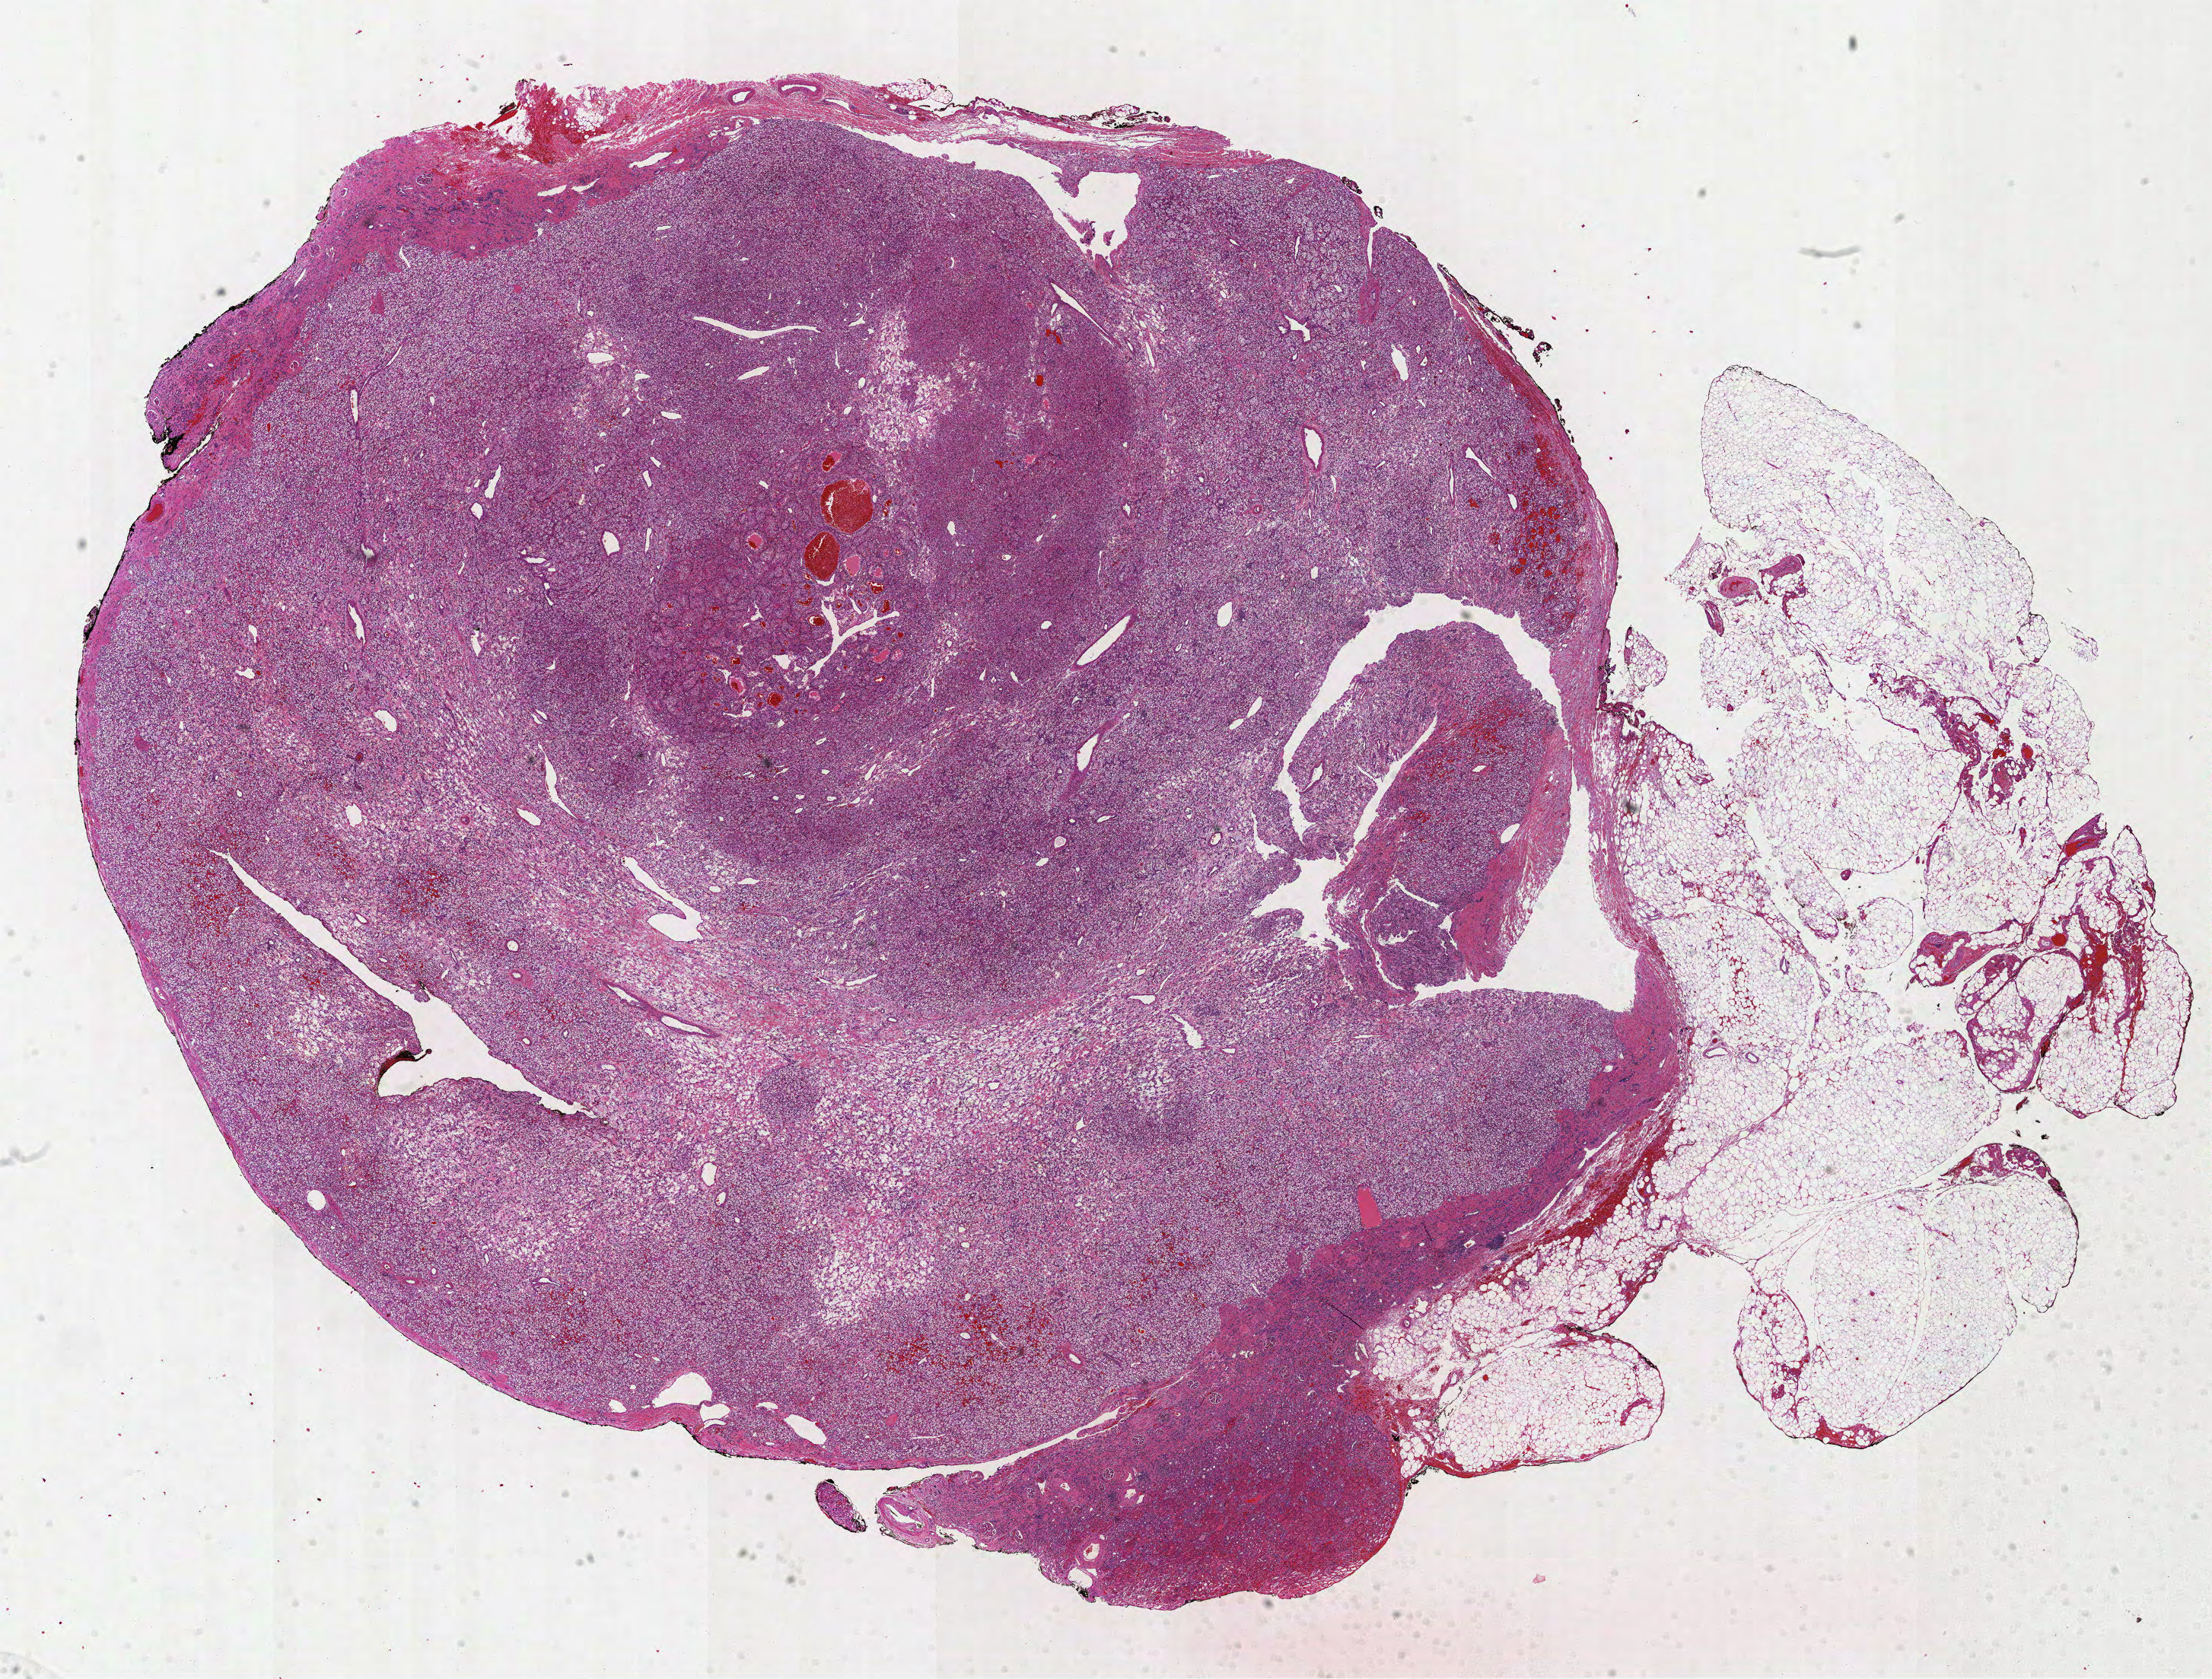
Digitized Hematoxylin and eosin (H&E) stained tissue section (whole slide) — low-resolution overview of the scanned area, about 23.4 x 17.8 mm (from a 40x scan), formalin-fixed paraffin-embedded (FFPE) diagnostic section, primary tumour sample from the kidney. Patient: female, age at initial diagnosis 67 years. Histologic grade: G2 (moderately differentiated).
- AJCC pathologic stage: I
- laterality: right
- histologic diagnosis: Clear cell adenocarcinoma, NOS